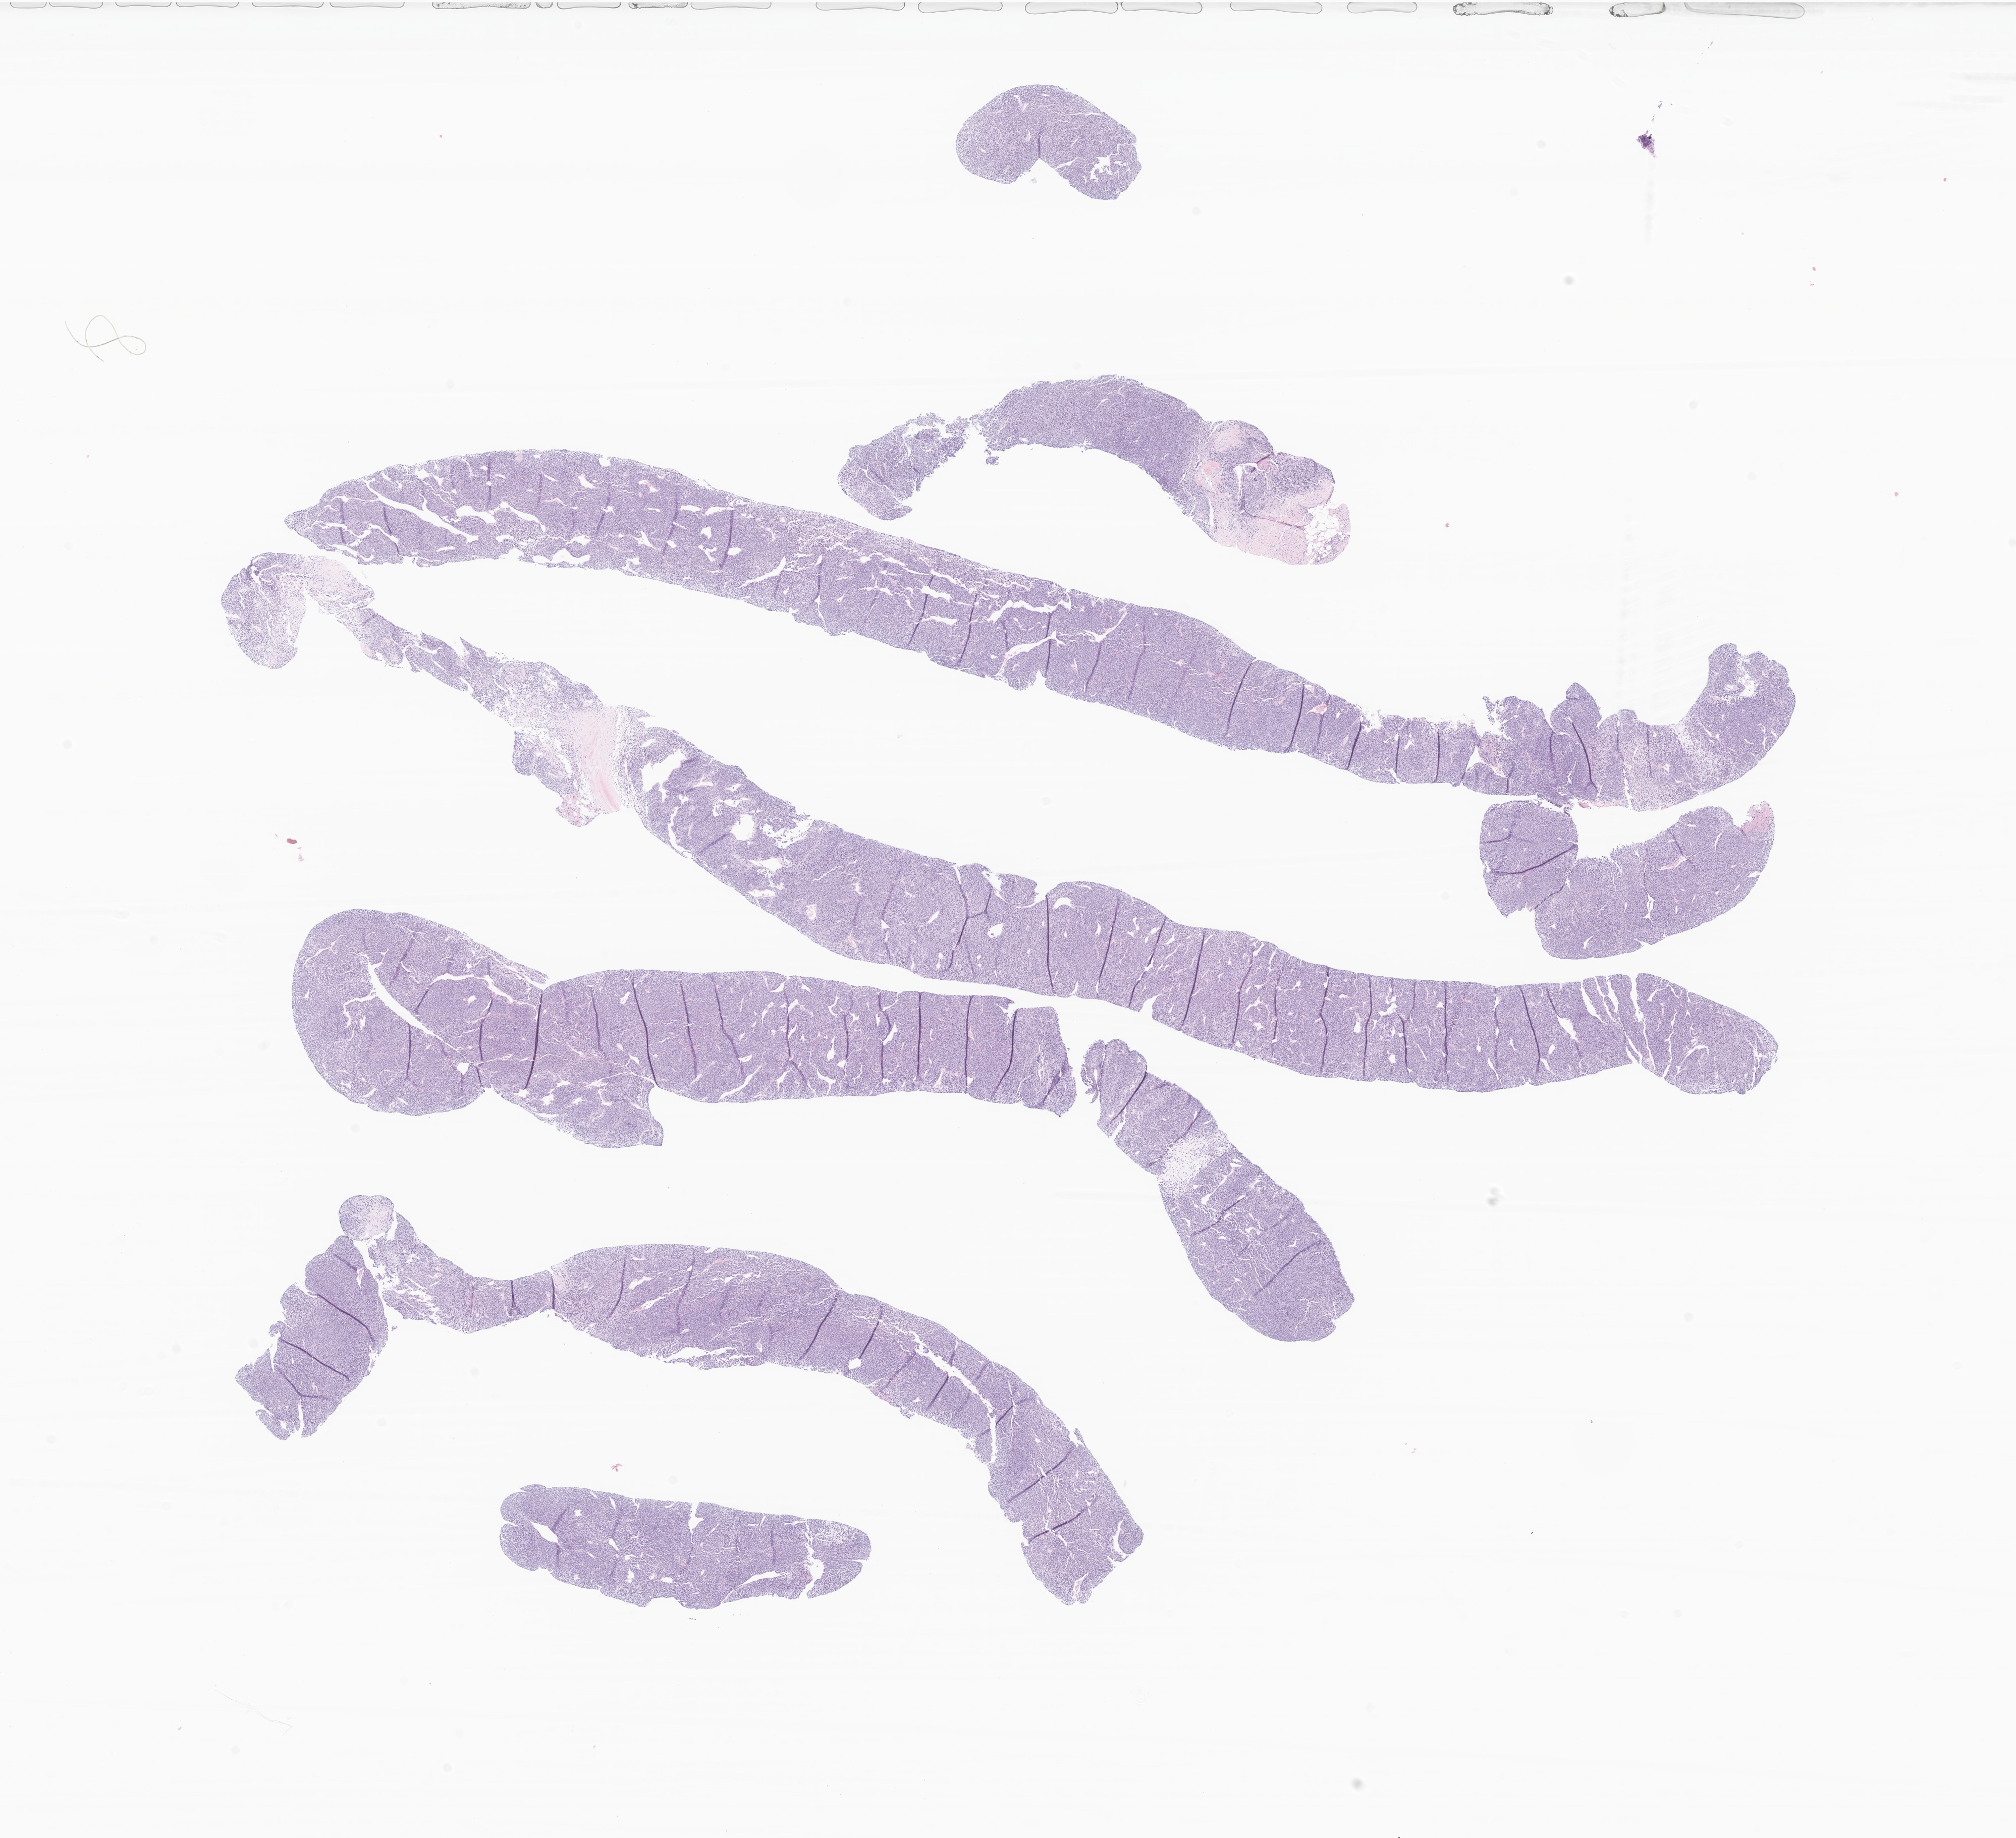
Digitized haematoxylin and eosin-stained section of tumor tissue from the soft tissue of lower extremity, low-resolution overview of the scanned area, about 16.8 x 15.4 mm. FFPE section. Patient female; age 151 months (12 years 7 months).
Recorded diagnosis: Sarcoma, NOS.